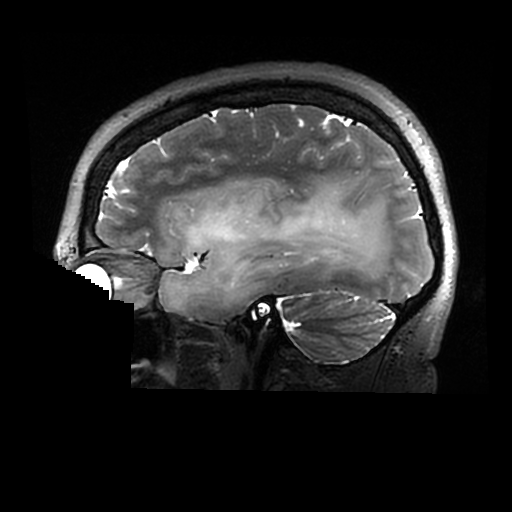
Brain MRI from a brain-tumour surgery series, one sagittal slice. Slice 207 of 320 in the series (ordered by position). 0.6 mm slice thickness. 512 × 512 image matrix, field of view 240 × 240 mm. Case-level facts recorded for this patient, not image findings: histopathology: Astrocytoma; WHO grade: 2; IDH mutation: yes.
Structures marked on this image (expert manual segmentation):
- tumour: box from (x=159, y=180) to (x=388, y=312) px